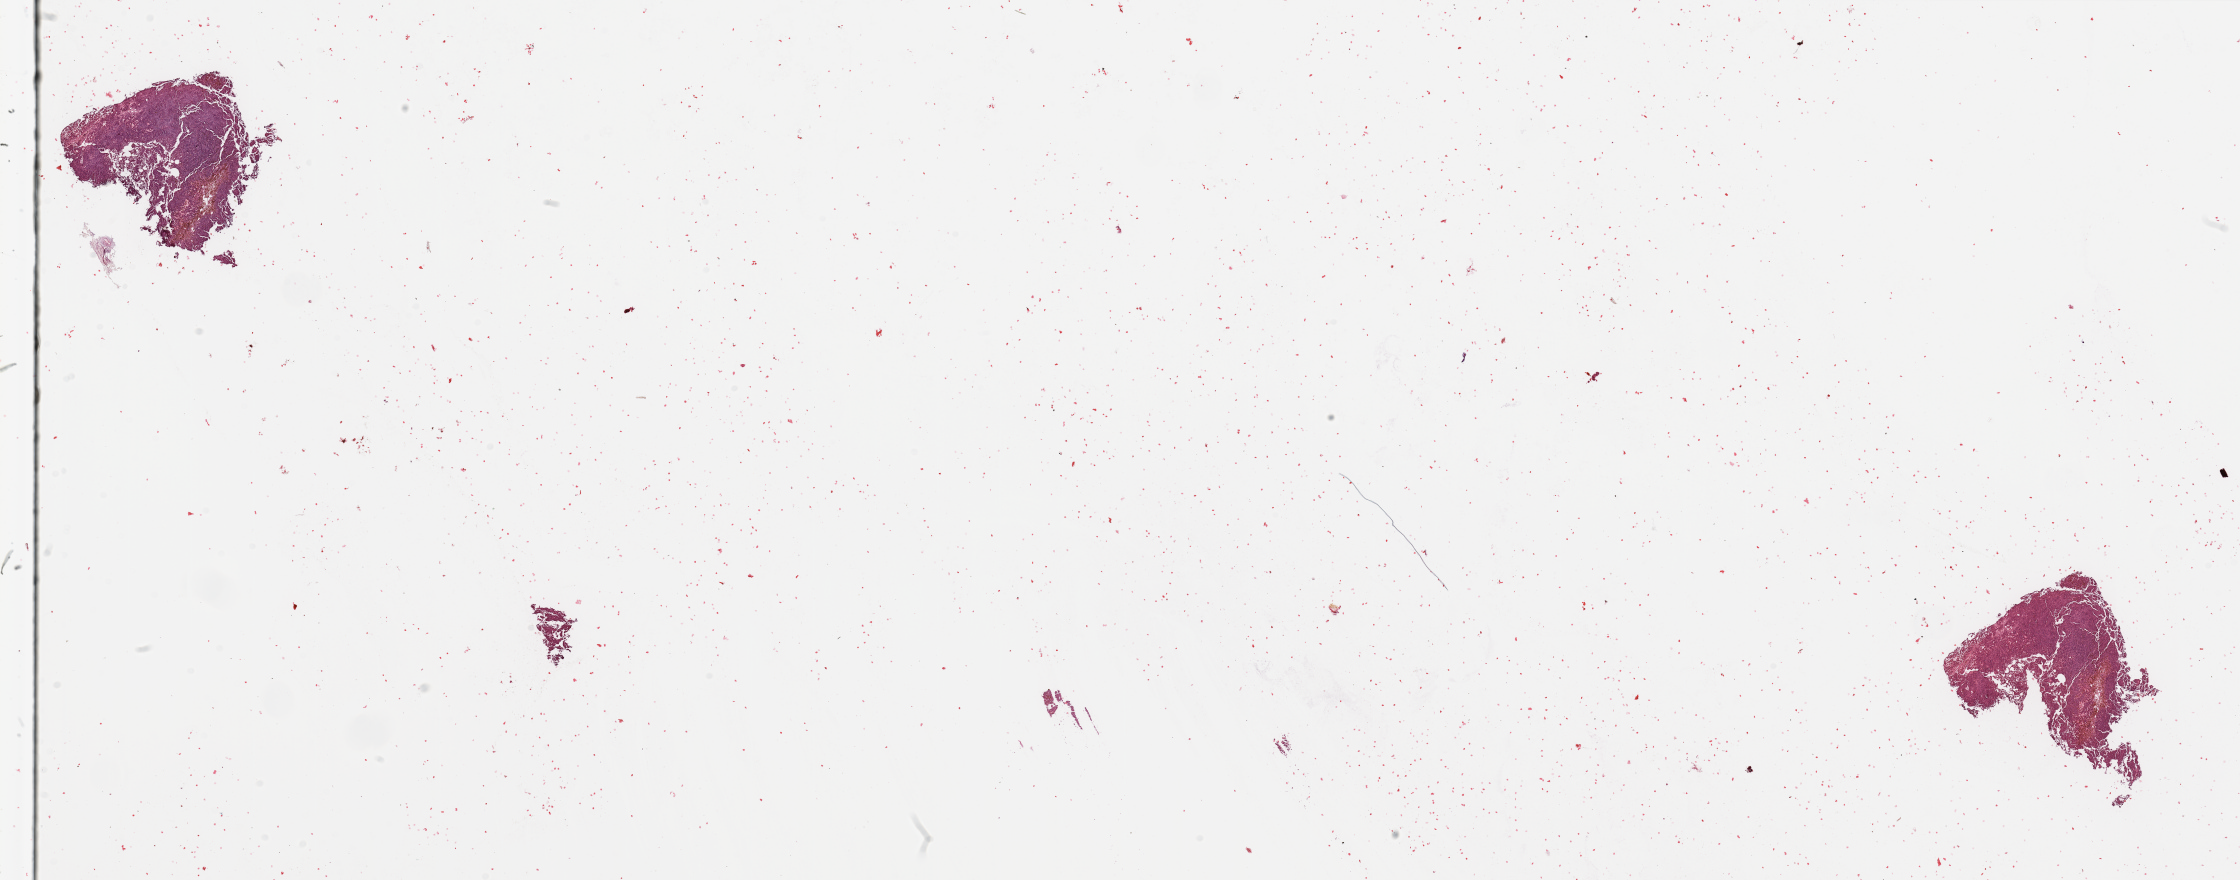
Digitized H&E tissue section (whole slide), shown as a low-resolution overview of the whole scanned area (about 35.4 x 13.9 mm); tumour tissue sample, sampled site: lymph node. Patient: male, age 76 years. Pathologist review of this section (percent, as recorded): tumour nuclei 90%, necrosis 2%.
This section: metastatic tumour tissue. Patient diagnosis: Malignant melanoma, NOS.